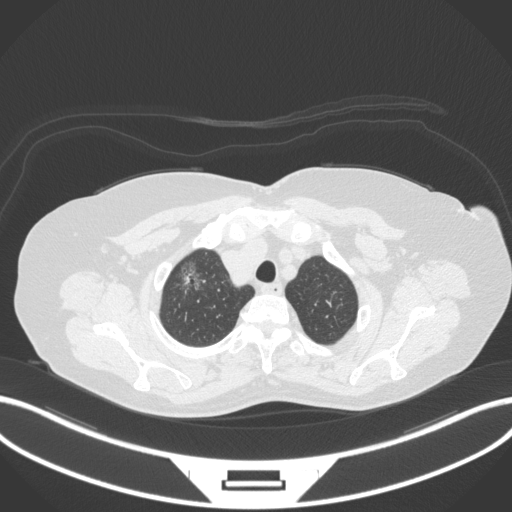
Chest CT, one axial slice; position 306 of 365 along the scan axis; reconstruction kernel B31f; 120 kVp; lung window (W 1500 / L -600 HU); 512 × 512 image matrix, field of view 400 × 400 mm. Female patient, age 62 years. Case-level facts recorded for this patient, not image findings: clinical TNM (as recorded): T1c N0 M0.
Annotated regions visible in this slice (rectangle marked by the reading radiologist):
- lung tumour (recorded histology: adenocarcinoma): bounding box [x1, y1, x2, y2] px = [170, 254, 212, 300]